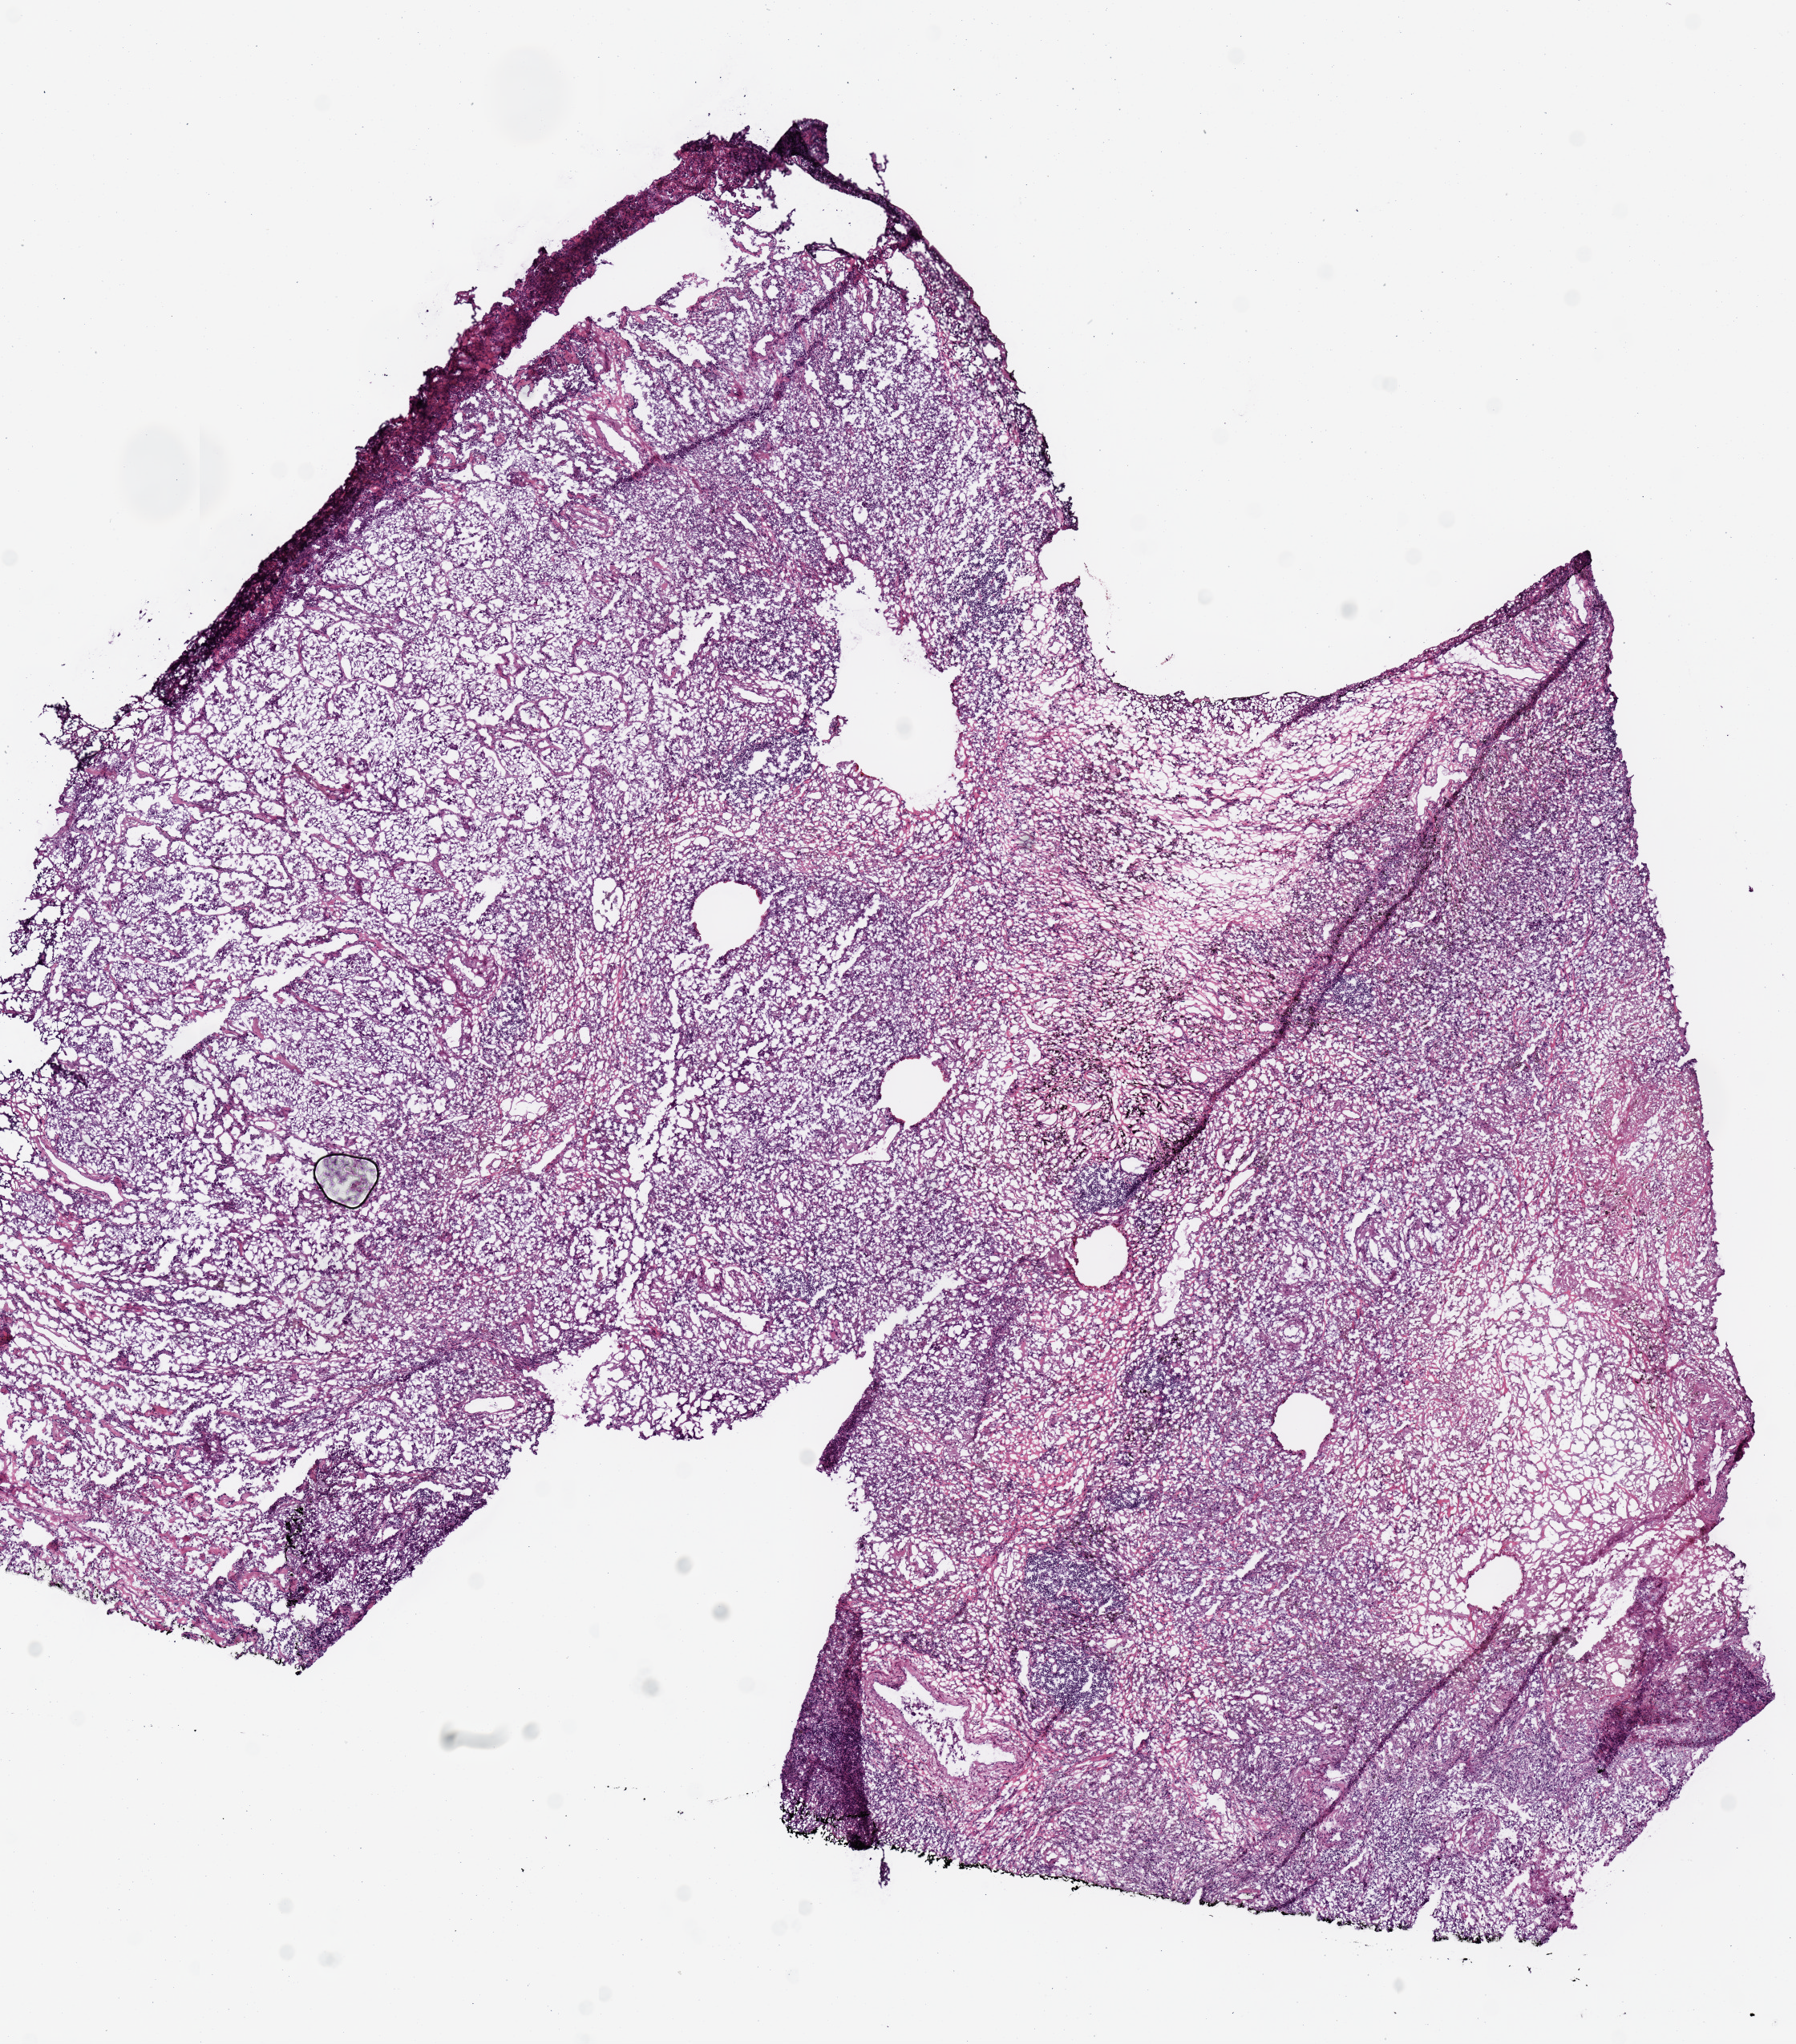
Whole-slide histology image, Hematoxylin and eosin (H&E) stained — low-resolution overview of the scanned area, about 8.9 x 10.1 mm (slide scanned at 20x). Frozen section. Sample: primary tumour, lung. Patient: male, age at initial diagnosis 54 years. Composition of this section per pathologist review: tumour cells 94%, tumour nuclei 80%, normal cells 0%, stromal cells 4%, necrosis 2%. Inflammatory infiltration, as recorded: lymphocyte infiltration 5%, monocyte infiltration 0%, neutrophil infiltration 0%.
TNM: T2 N0 MX. Diagnosis: Adenocarcinoma, NOS (lower lobe, lung). AJCC pathologic stage: IB.